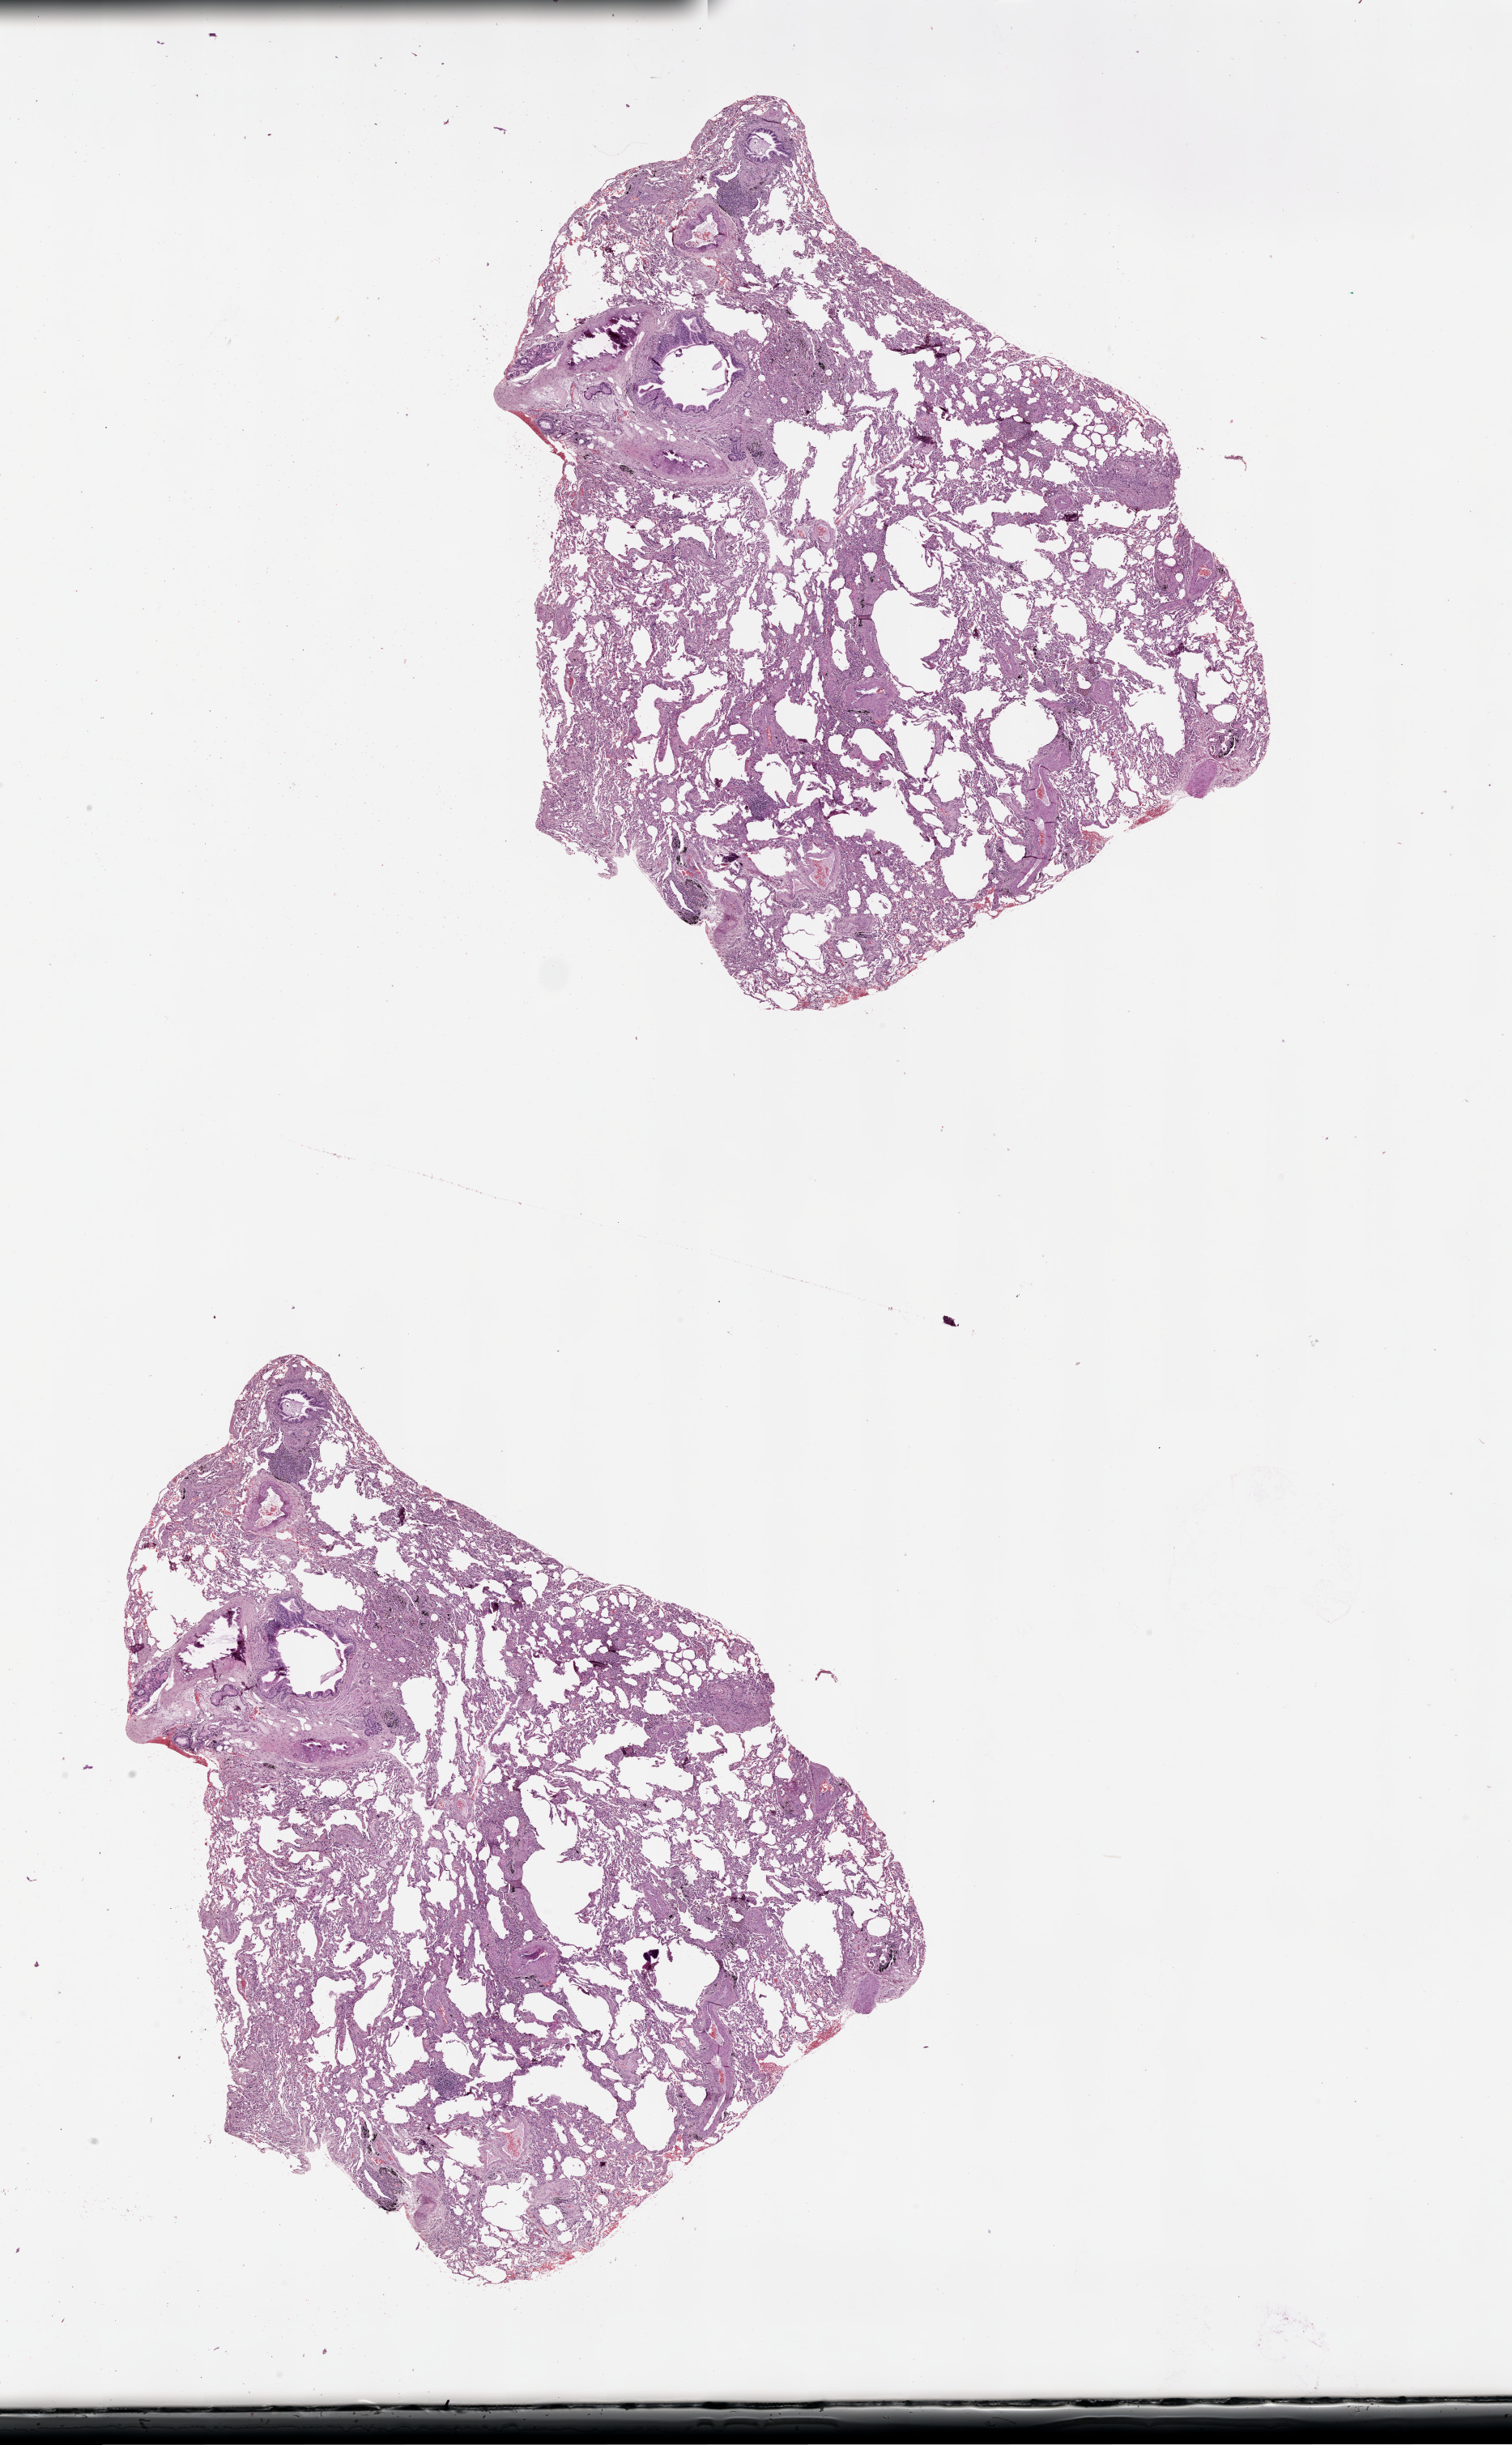
Digitized H&E-stained tissue section (whole slide), a low-resolution overview of the entire scanned area, about 15.0 x 24.3 mm (from a 20x scan); lung, normal (non-tumour) tissue. Female, 60 y/o.
This section: normal (non-tumour) tissue from the same patient. Patient diagnosis (cohort enrolment): squamous cell carcinoma (lung).